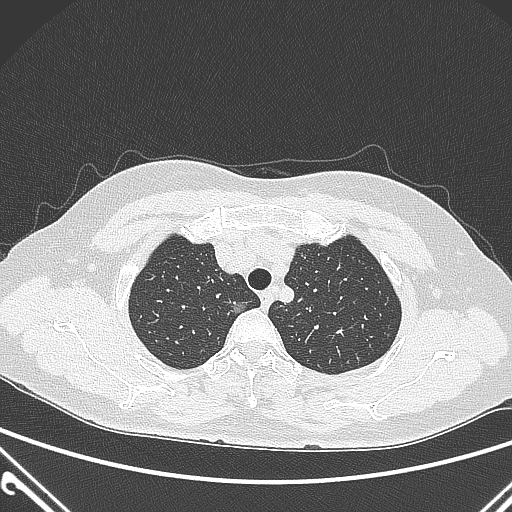
Chest CT, one axial slice; slice 236 of 300 in the series (ordered by position); lung window (W 1500 / L -600 HU); 512 × 512 image matrix, field of view 350 × 350 mm. Female patient, age 54 years. From the clinical record (not read from this slice): clinical TNM (as recorded): T1a N0 M0.
Annotated regions visible in this slice (rectangle marked by the reading radiologist):
- lung tumour (recorded histology: adenocarcinoma): bounding box [x1, y1, x2, y2] px = [228, 292, 263, 330]